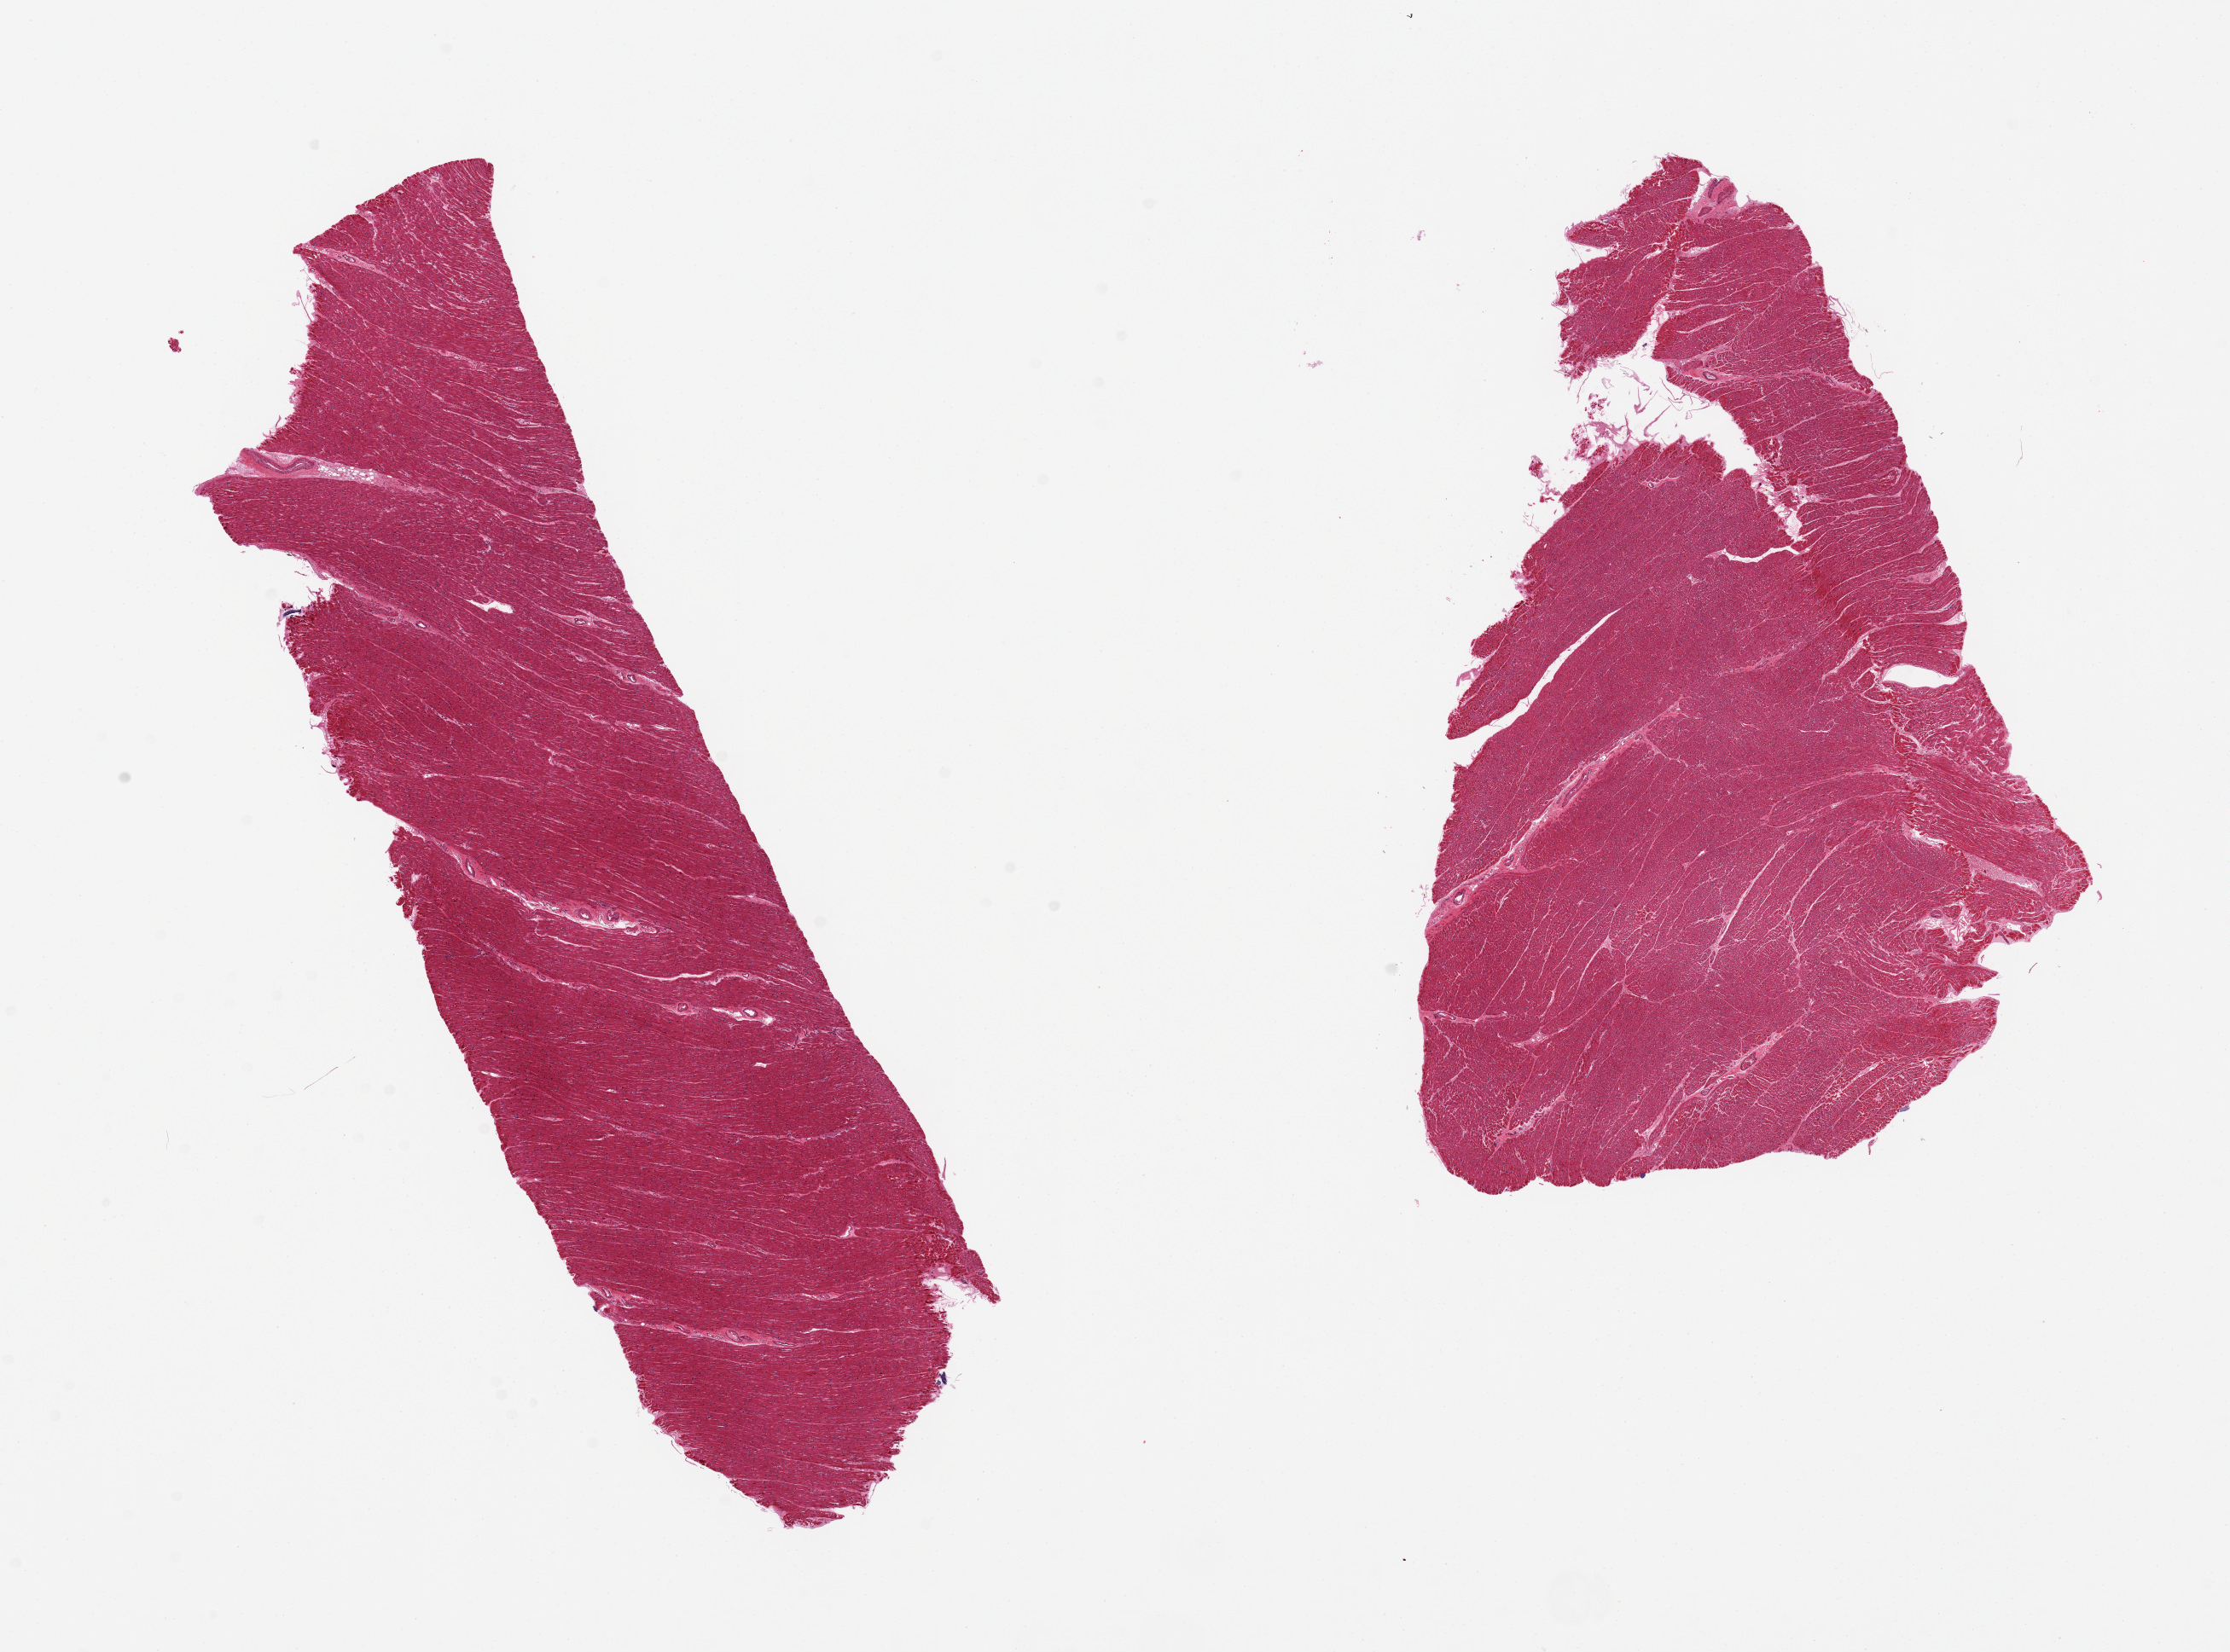
Whole-slide image, haematoxylin and eosin stain — low-resolution overview of the scanned area, about 20.7 x 15.3 mm; PAXgene-fixed paraffin-embedded (PFPE) section; section of heart (target tissue); tissue donor sample. Male donor.
Review note (as recorded): 2 pieces; enlarged nuclei.